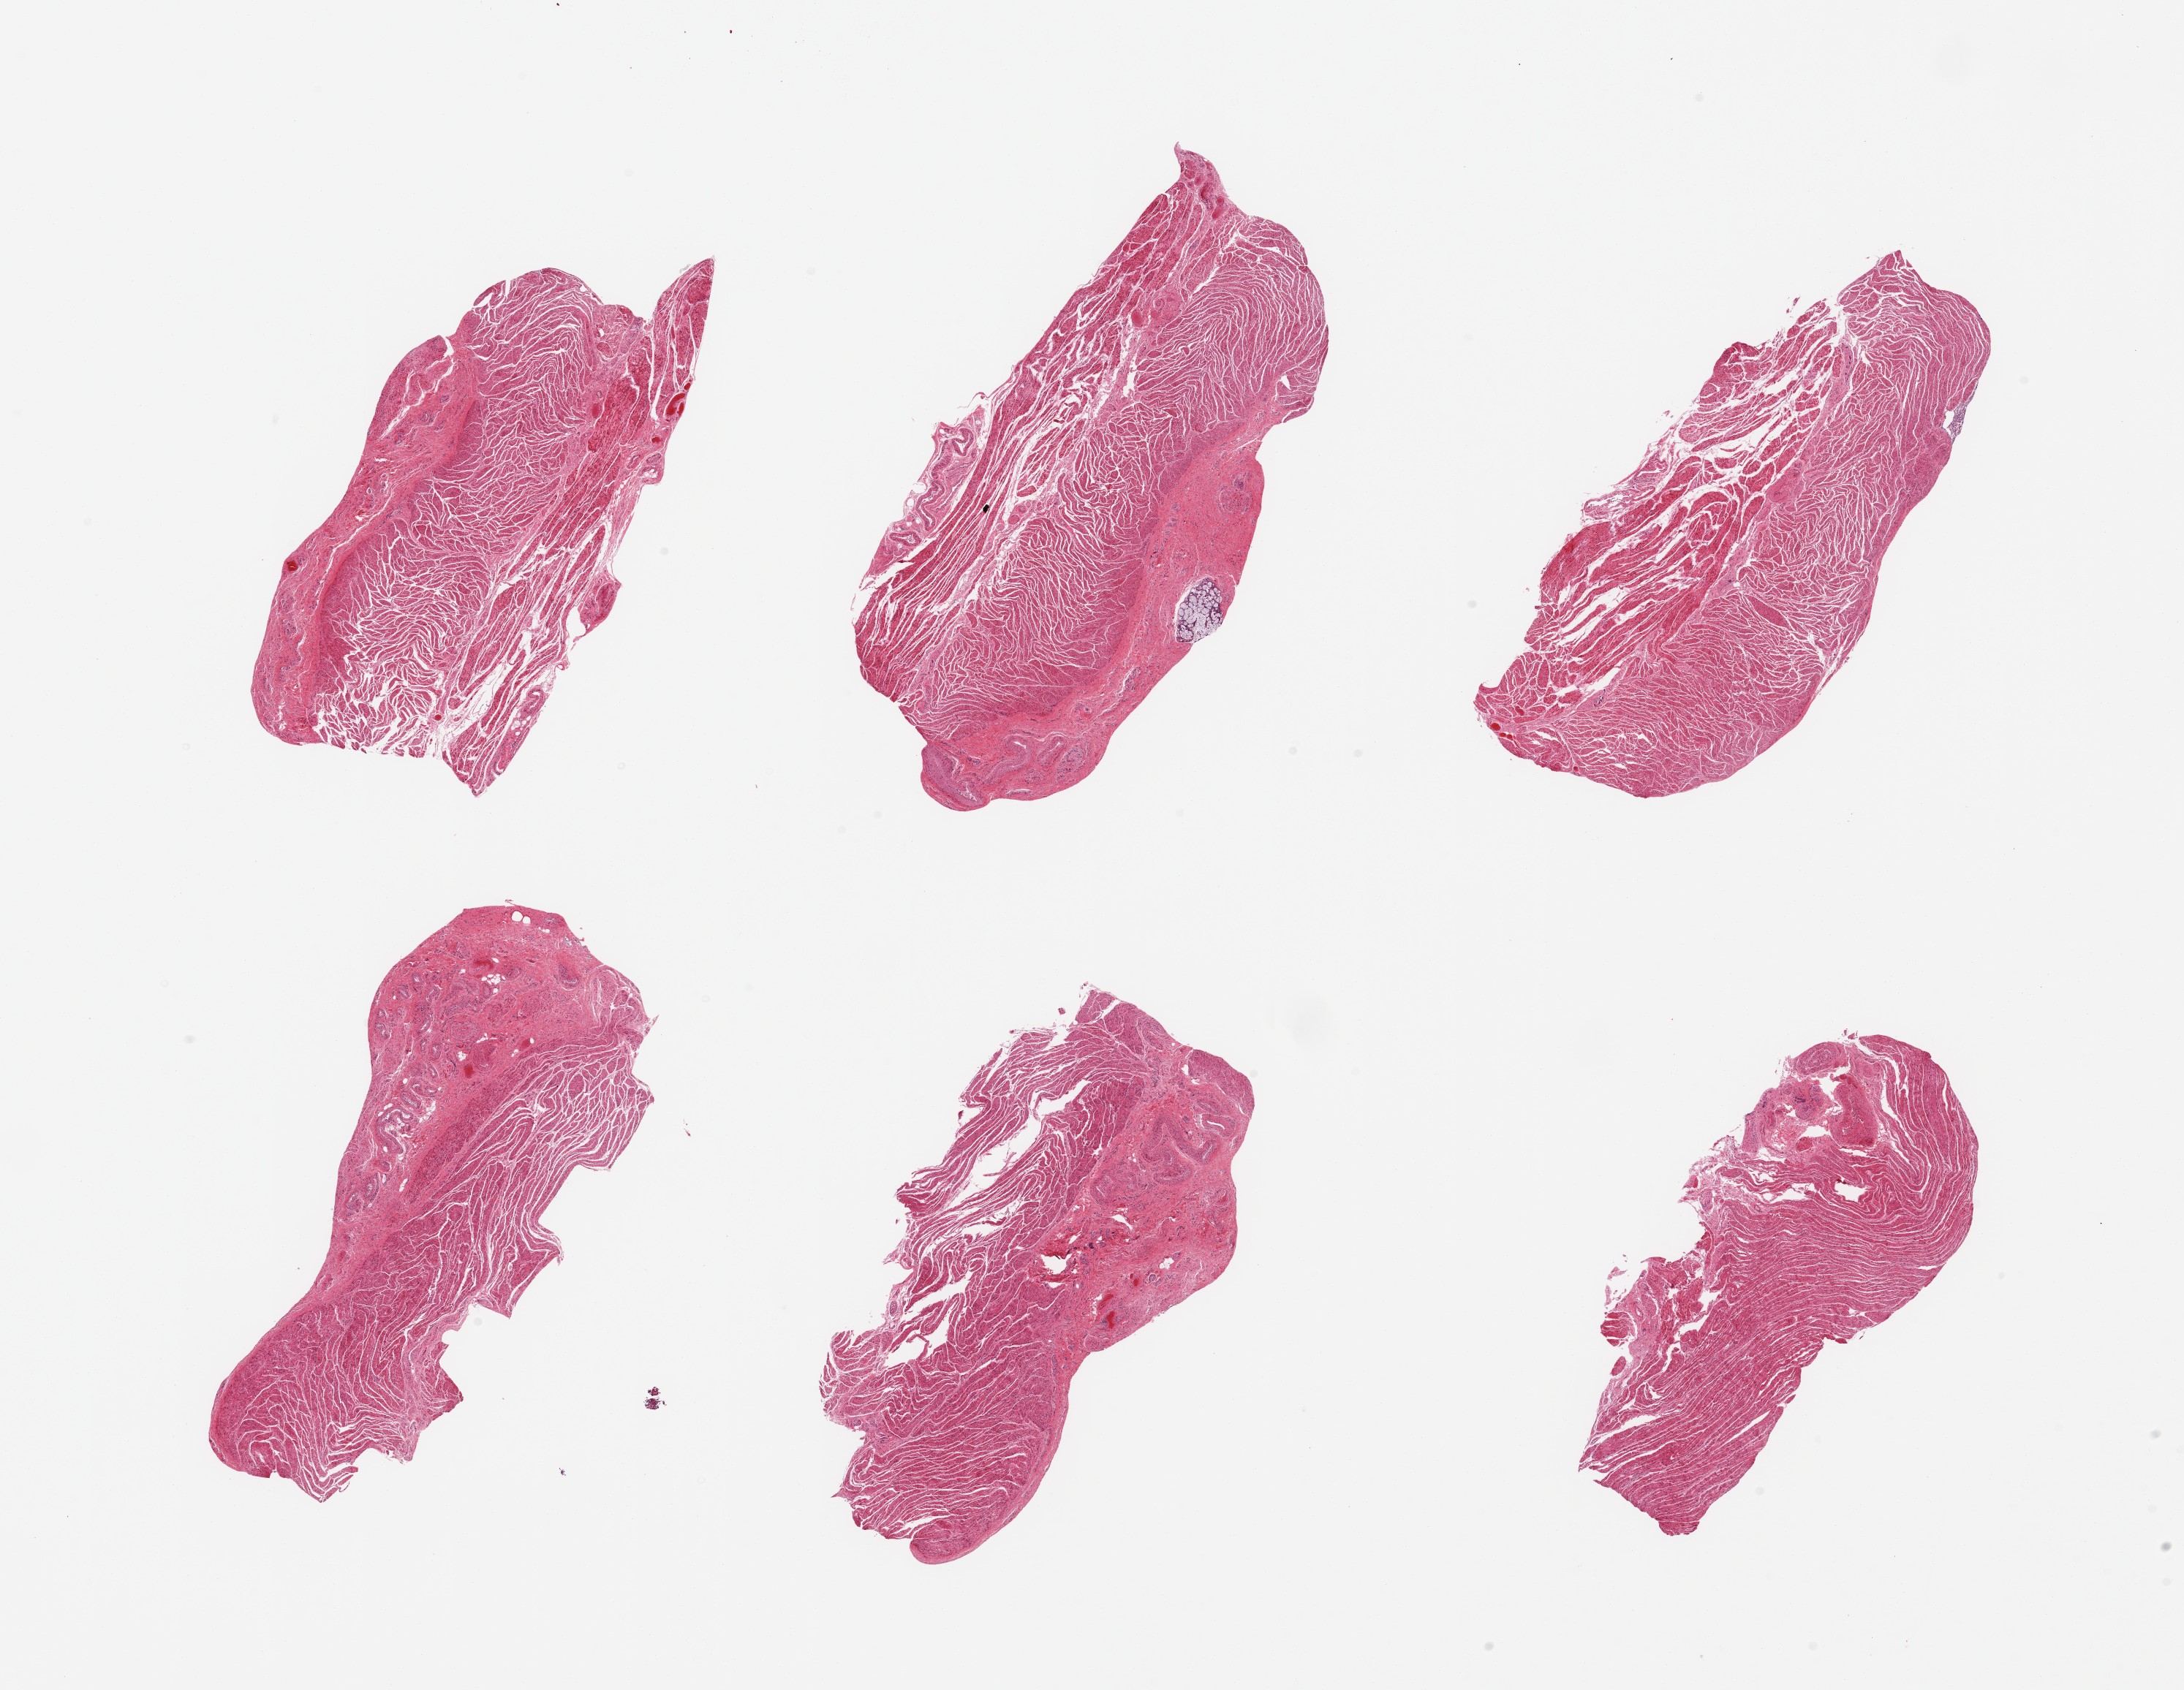
Whole-slide image, H&E stain, brightfield — shown as a low-resolution overview of the whole scanned area (about 23.6 x 18.3 mm, from a 20x scan), PAXgene-fixed paraffin-embedded (PFPE) section, sampled site (target tissue): gastroesophageal junction, donor tissue sample.
* reviewer comment on this tissue sample: 6 pieces; target muscularis with submucosa, foci of submucosal glands/detached cellular debris